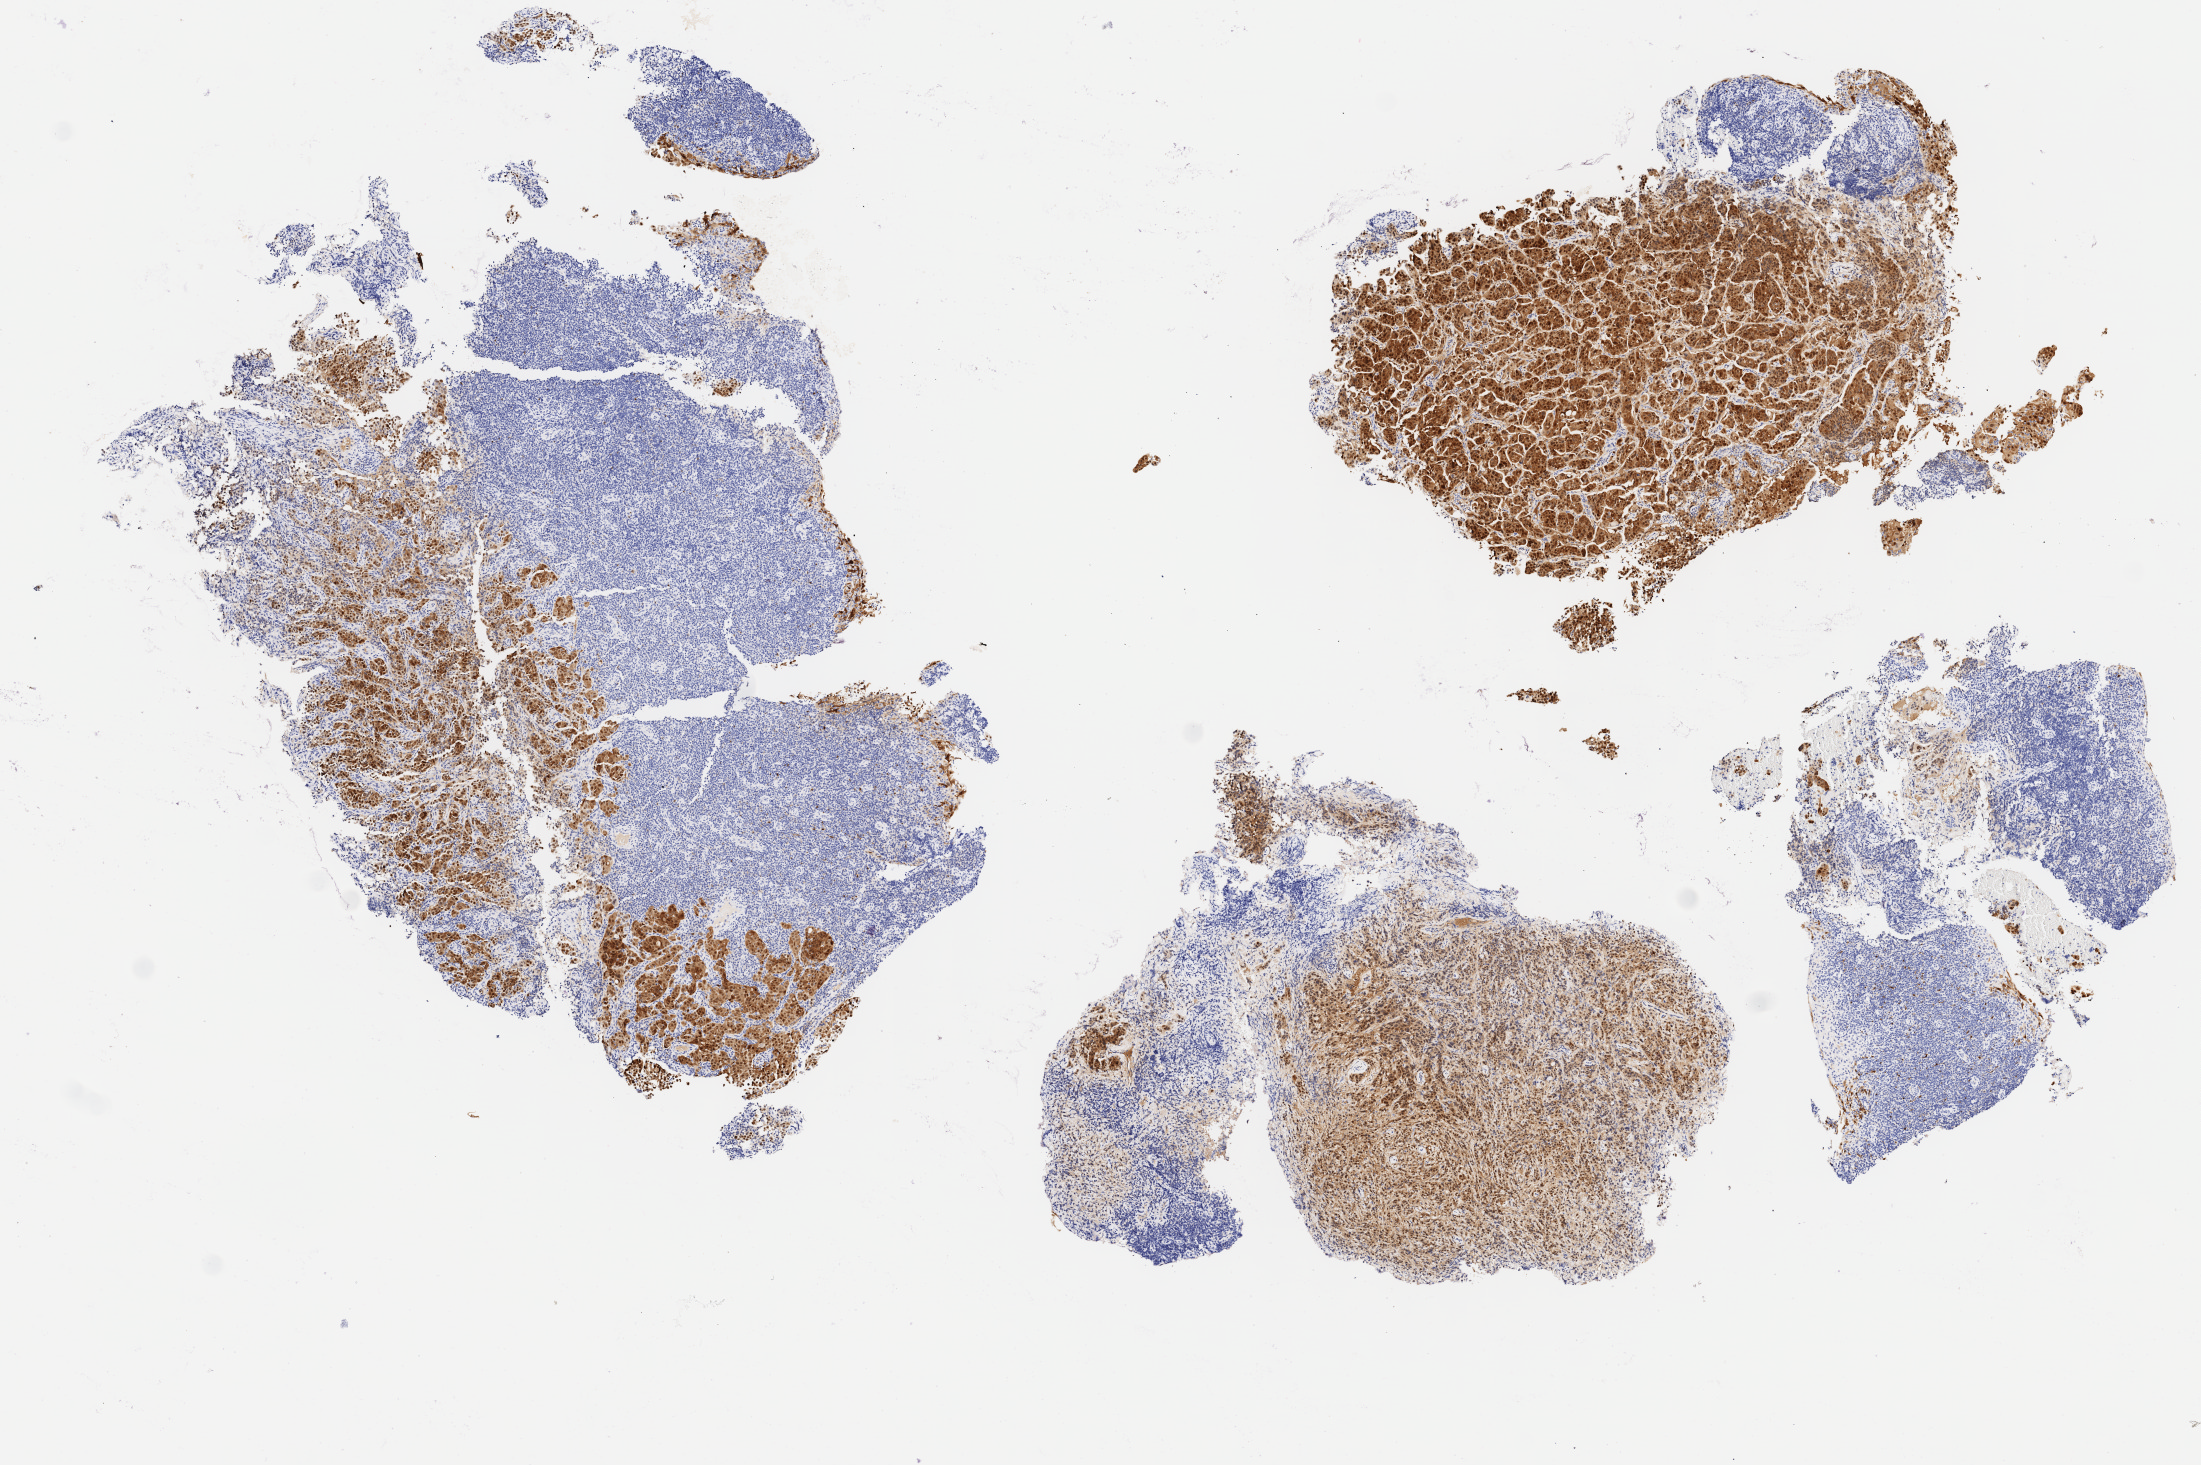
Whole-slide image, immunohistochemical stain for p16 (p16INK4a), a low-resolution overview of the entire scanned area, about 8.8 x 5.8 mm; tumor tissue; site: cervix. Patient female; 54 years old.
Diagnosis: Adenocarcinoma, NOS.